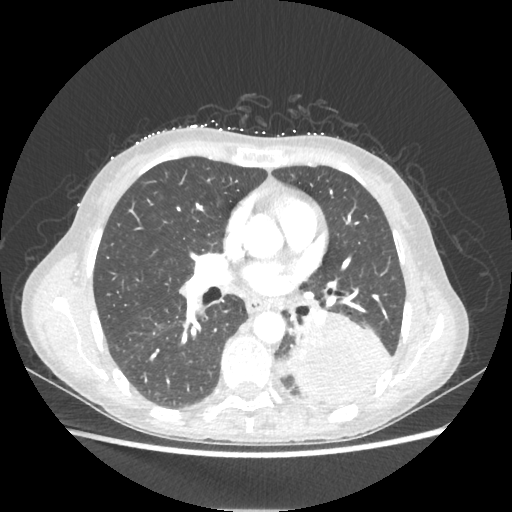
Chest CT, one axial slice. Slice 116 of 221 in the series (ordered by position). Lung window (W 1500 / L -600 HU). 1.25 mm slice thickness. 512 × 512 image matrix, field of view 360 × 360 mm. Patient: female, 53 years. Case-level facts recorded for this patient, not image findings: clinical TNM (as recorded): T3 N0 M0.
Annotated regions visible in this slice (bounding box drawn by a radiologist):
- lung tumour (recorded histology: adenocarcinoma): bounding box <287,309,392,406> (left, top, right, bottom; pixels)